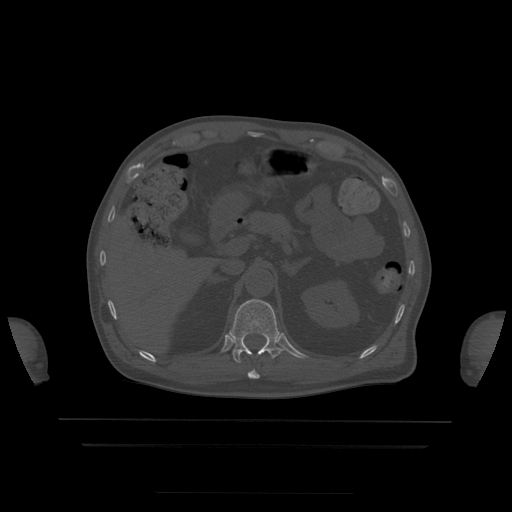
CT including the spine, one axial slice. Bone window (W 1800 / L 400 HU). 1.25 mm slice thickness. 512 × 512 image matrix, field of view 436 × 436 mm. Patient age 68 years. Case-level facts recorded for this patient, not image findings: primary cancer: urothelial.
Annotated regions visible in this slice (semi-automatic segmentation, software-assisted and operator-edited):
- T11 vertebra: box from (x=248, y=370) to (x=260, y=379) px
- T12 vertebra: (x=229, y=299)–(x=283, y=363)